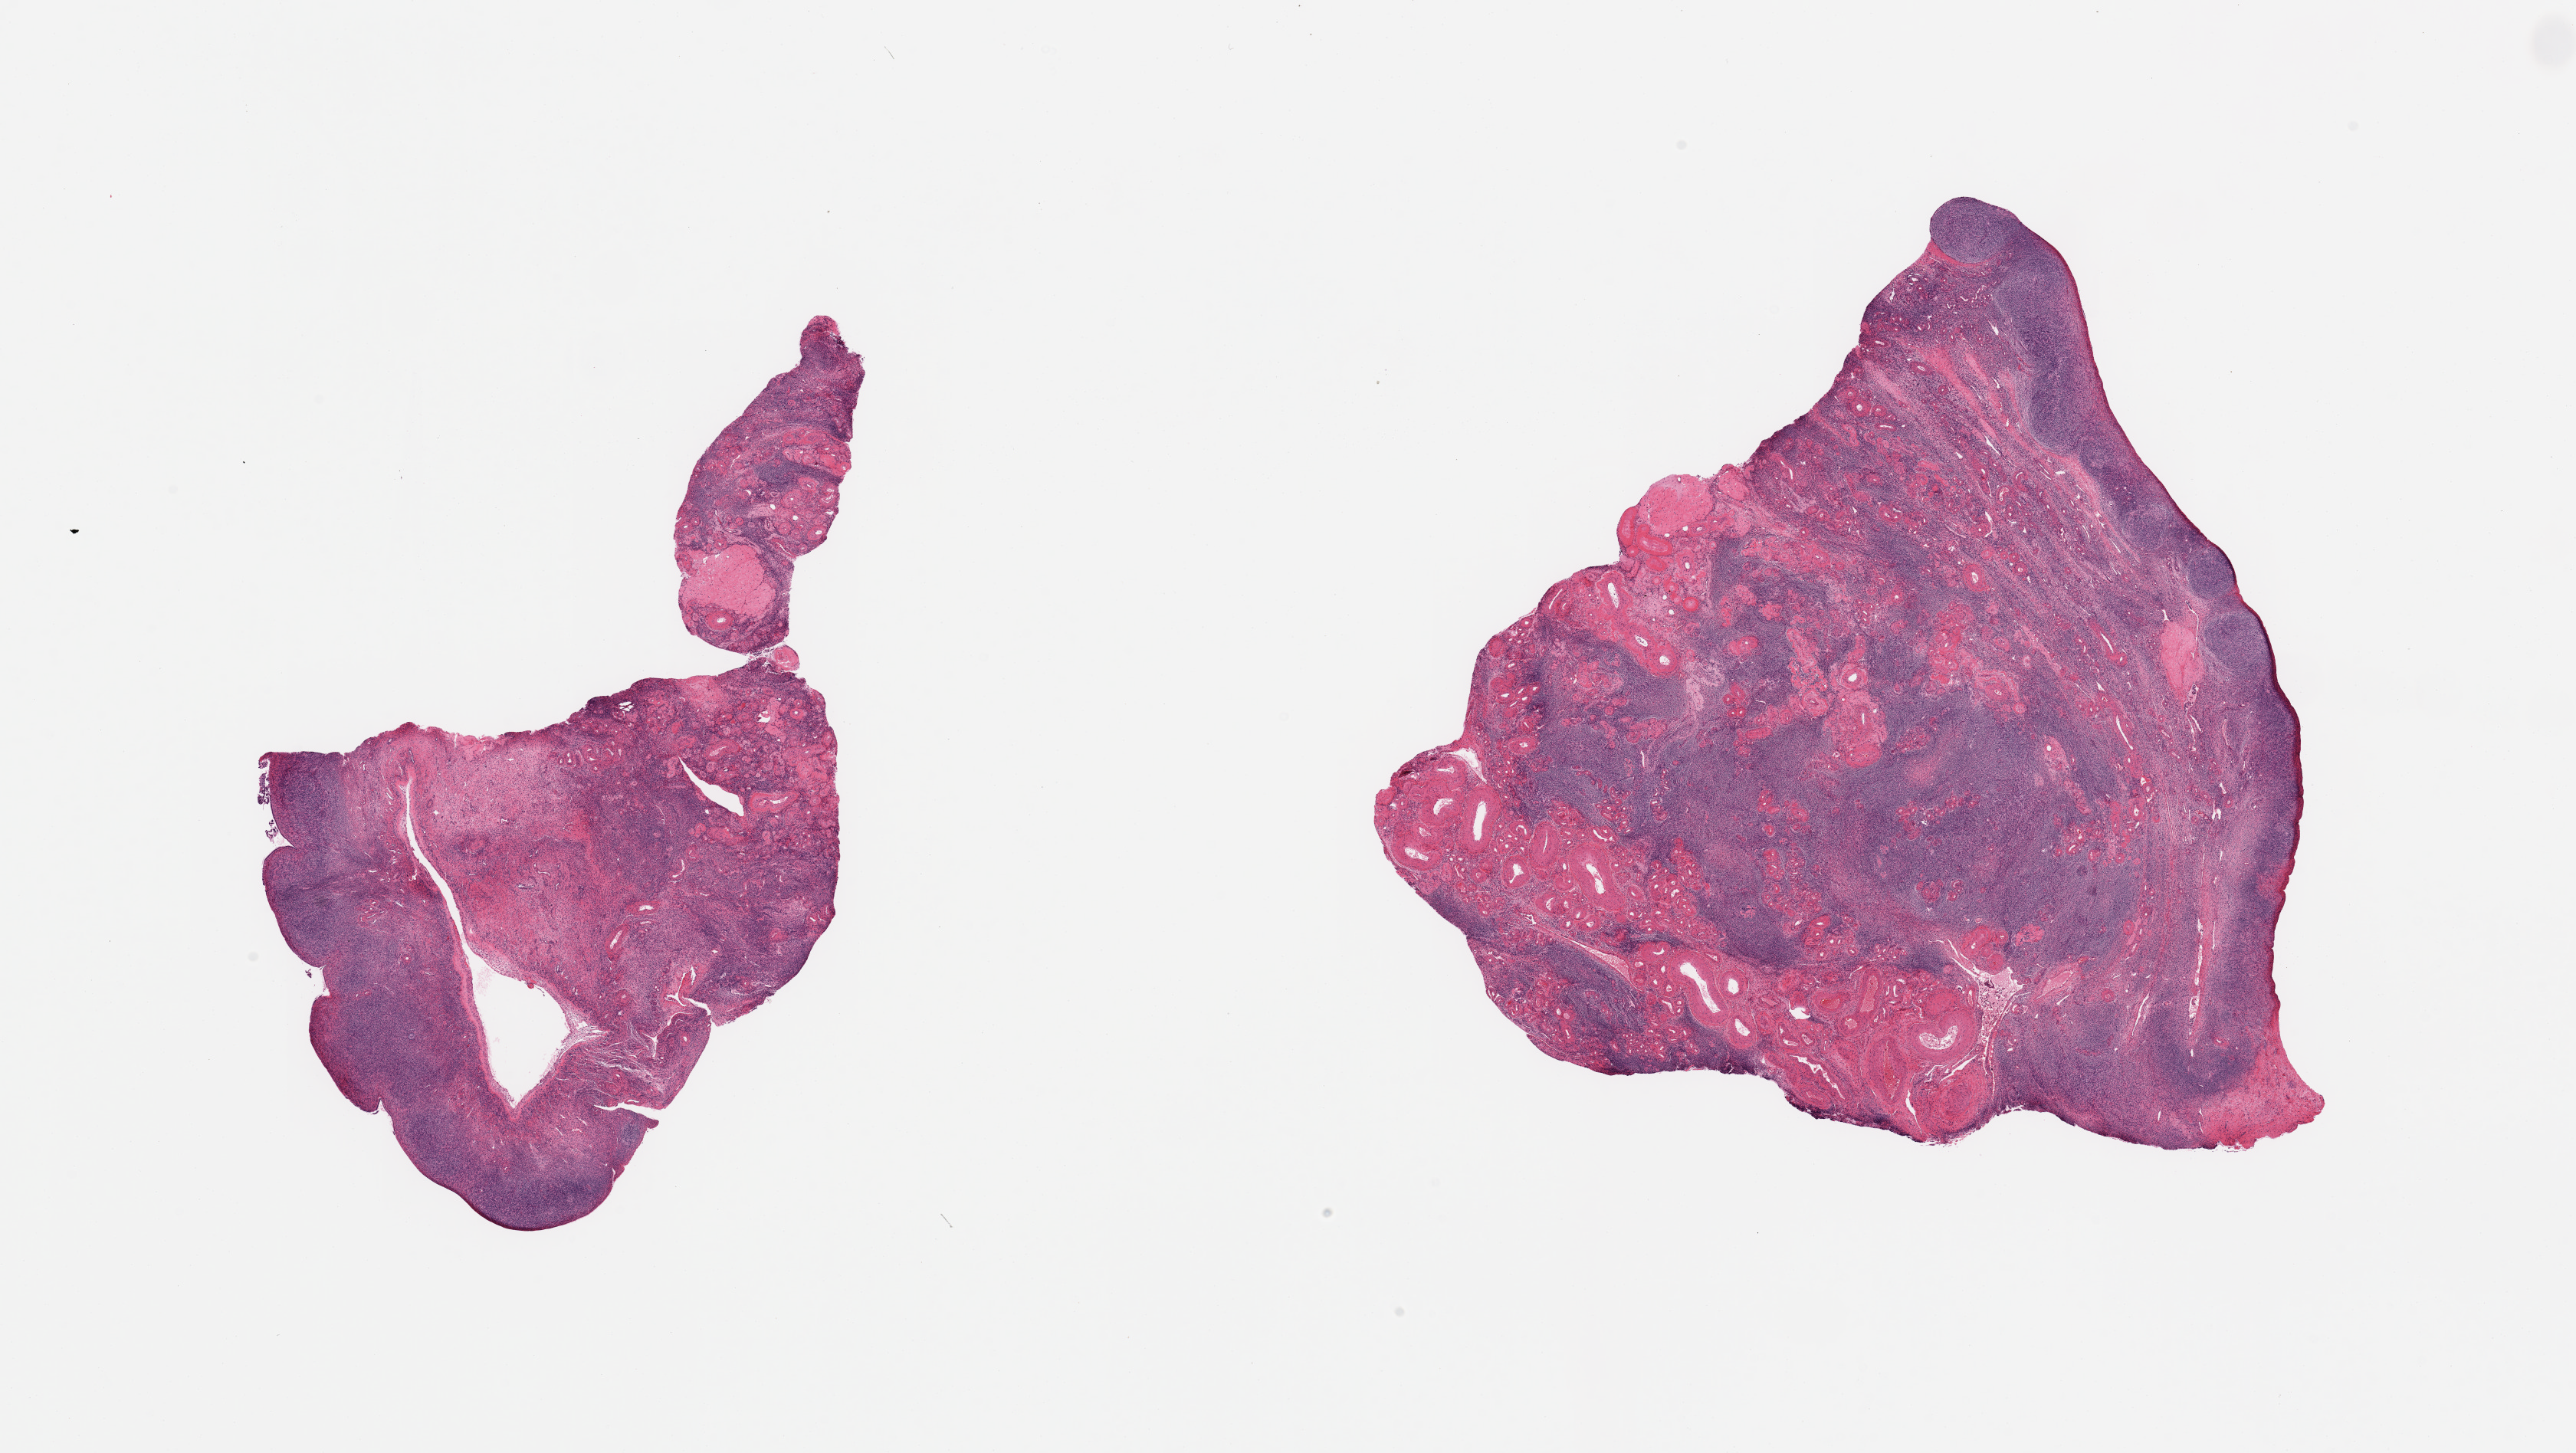
Hematoxylin and eosin (H&E) whole-slide image, shown as a low-resolution overview of the whole scanned area (about 26.6 x 15.0 mm), PAXgene-fixed, paraffin-embedded tissue, section of ovary (target tissue), donor tissue sample. Female donor.
• pathologist's review note for this sample: 2 pieces, typical post menopausal atrophy